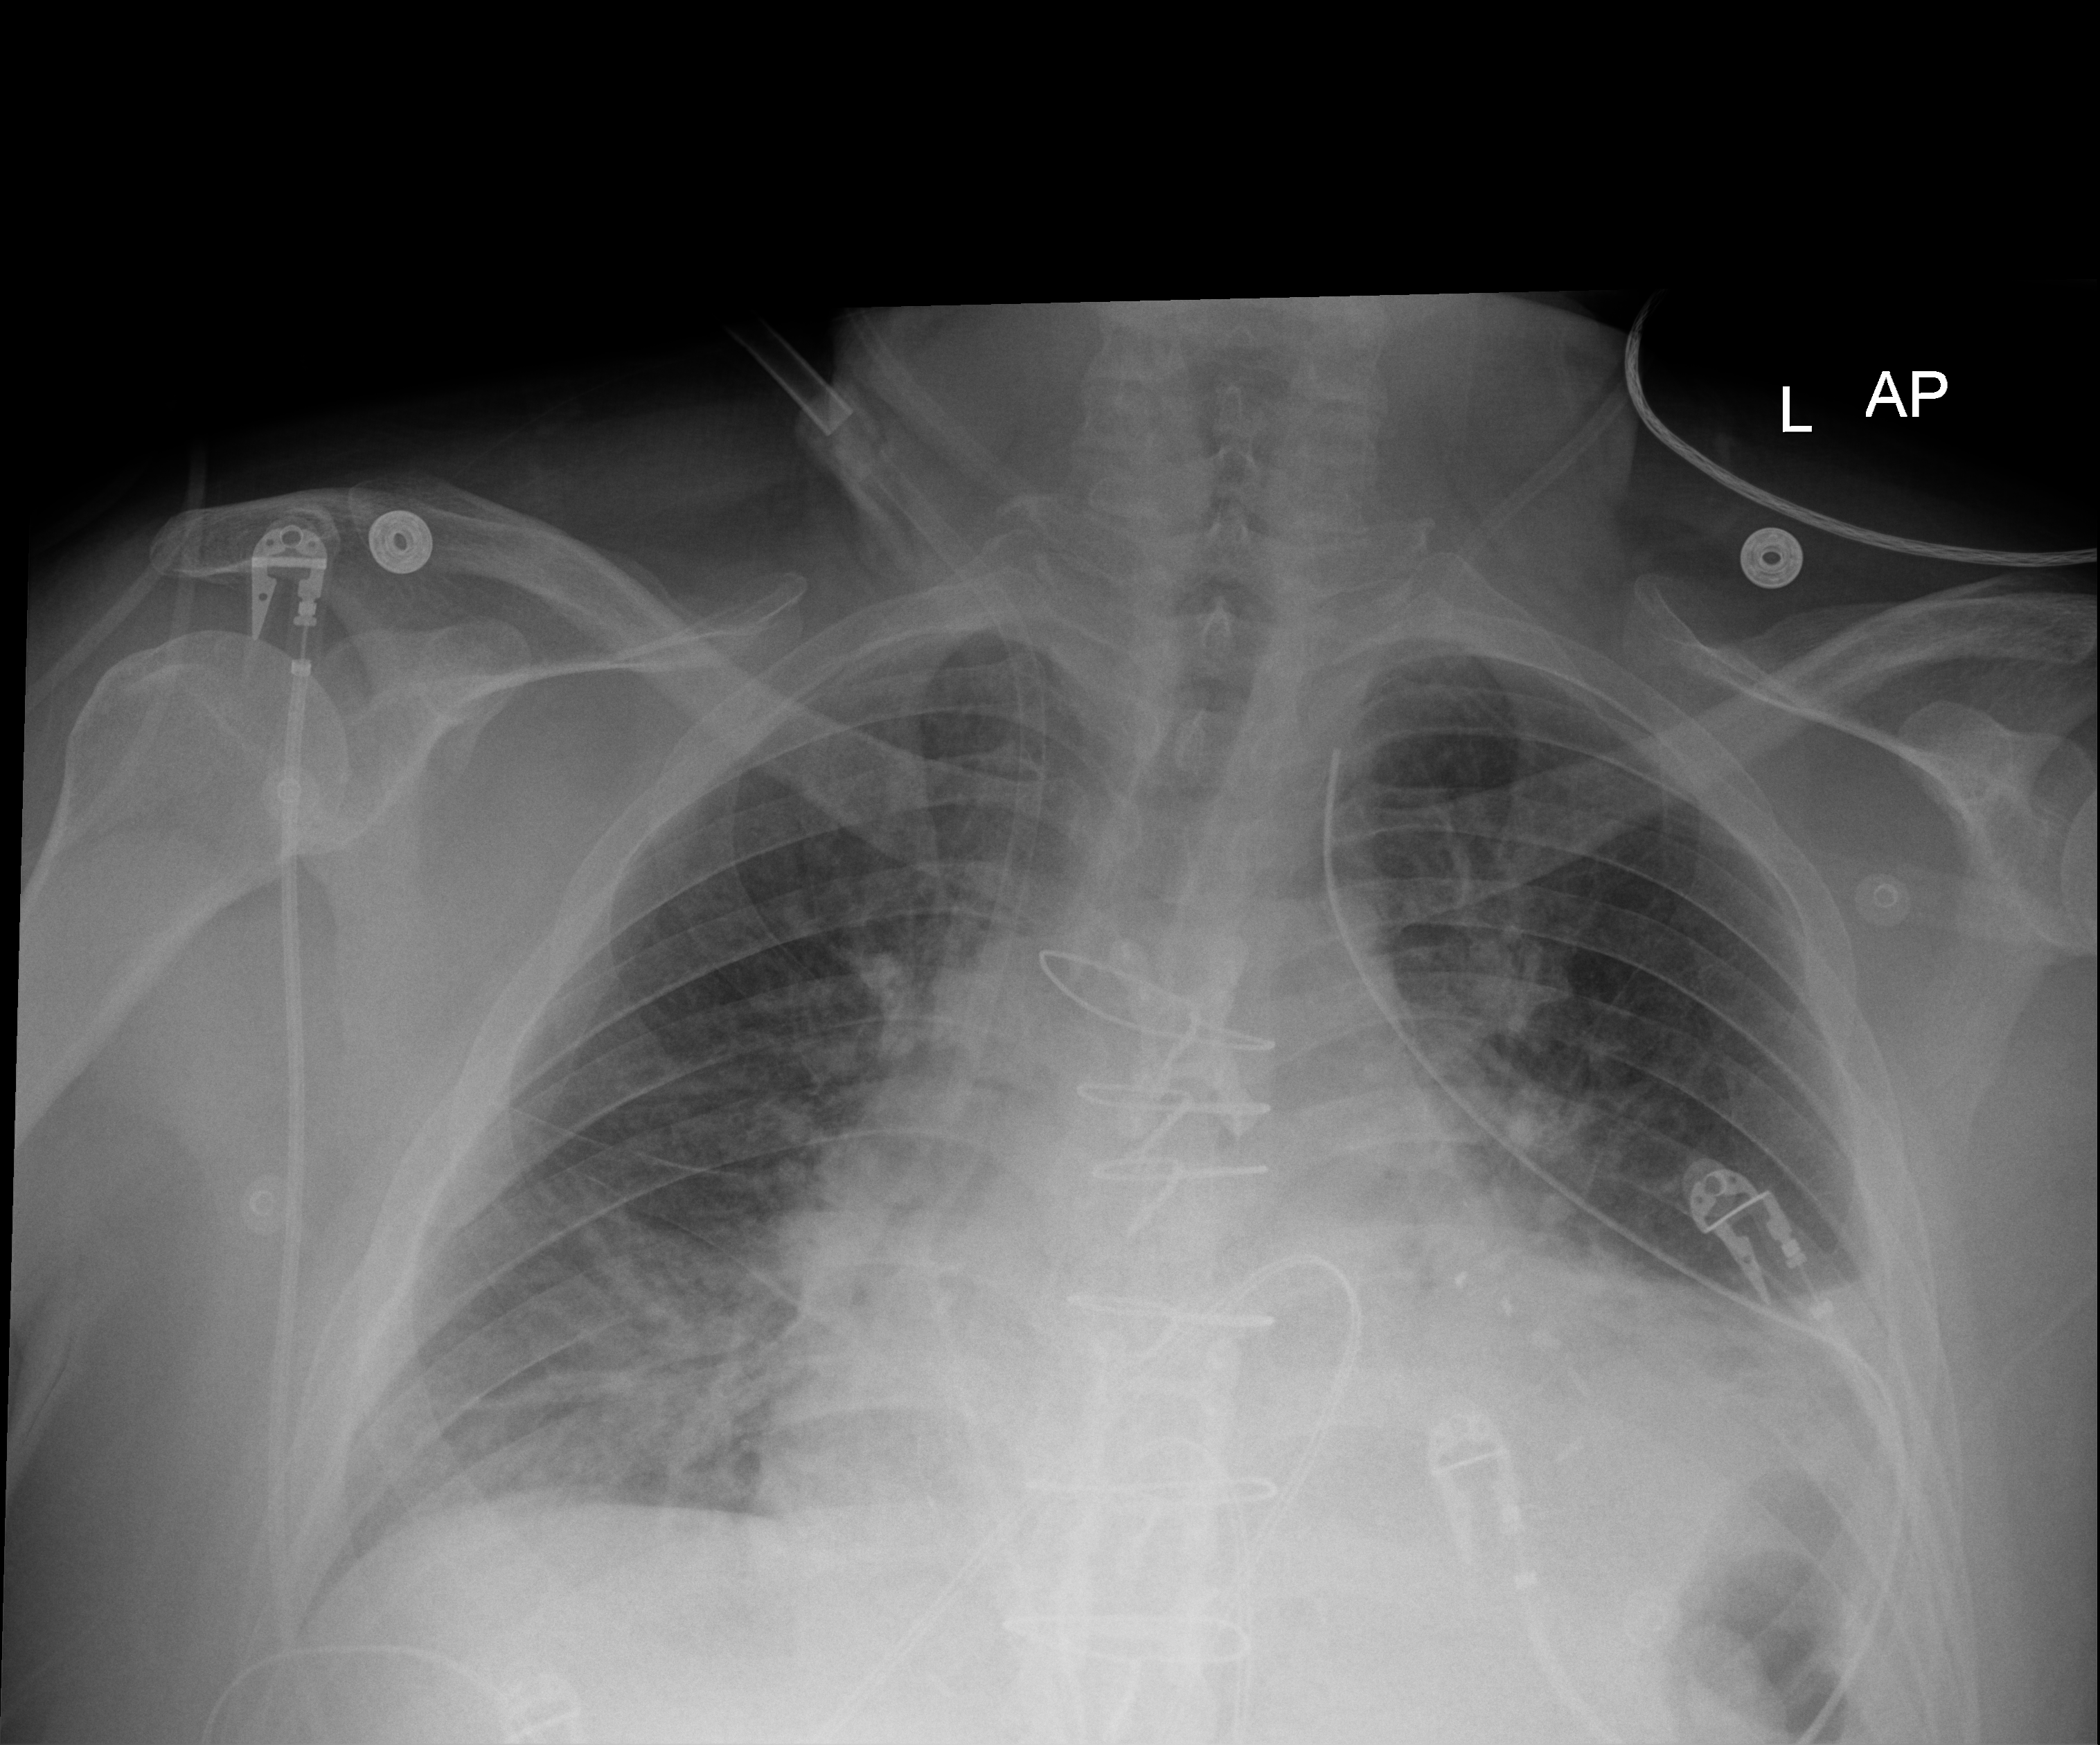
Bedside chest radiograph (digital radiography). Patient hospitalised with COVID-19; male, aged 18–59 years.
Hospital-stay facts (about this admission, not read from this image; timing relative to this image not recorded):
- length of hospital stay: 17 days
- mechanically ventilated during this hospital stay: no
- admitted to intensive care during this hospital stay: no